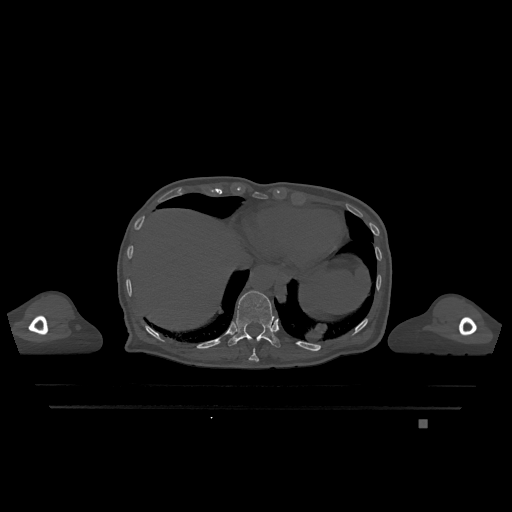
CT including the spine, one axial slice. Position 602 of 1317 along the scan axis. Bone window (W 1800 / L 400 HU). 0.5 mm slice thickness. 512 × 512 image matrix, field of view 500 × 500 mm. Female patient, age 74 years. Case-level facts recorded for this patient, not image findings: primary cancer: lung.
Annotated regions visible in this slice (semi-automatic segmentation, software-assisted and operator-edited):
- T10 vertebra: bounding box <249,348,259,362> (left, top, right, bottom; pixels)
- T11 vertebra: <228,290,280,348>